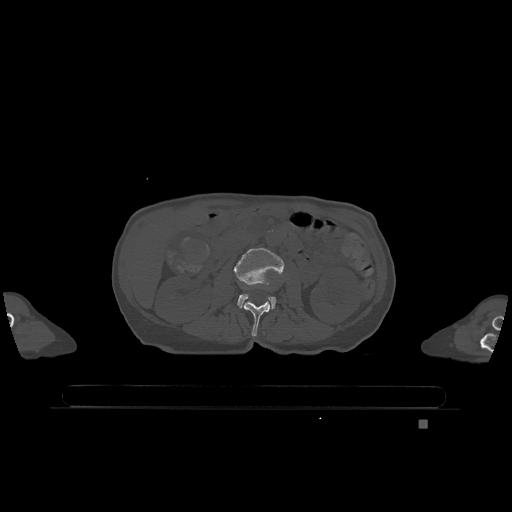
CT including the spine, one axial slice. Slice 391 of 1317 in the series (ordered by position). Bone window (W 1800 / L 400 HU). 0.5 mm slice thickness. 512 × 512 image matrix, field of view 500 × 500 mm. Patient: female, 74 years. Case-level facts recorded for this patient, not image findings: primary cancer: lung; vertebrae with lytic lesions (as recorded): T1, T4, T5, T6, L4, L5.
Structures marked on this image (semi-automatic segmentation, software-assisted and operator-edited):
- L2 vertebra: box from (x=244, y=301) to (x=270, y=337) px
- L3 vertebra: (x=234, y=248)–(x=284, y=309)